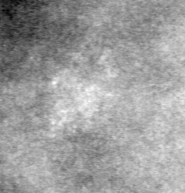
Crop from a digitized film mammogram around one marked abnormality, left breast, CC view, BI-RADS breast density category 4 (scale 1–4).
Finding: calcifications, morphology pleomorphic, distribution clustered; BI-RADS assessment category 4; subtlety rating 1 on a 1 (subtle) to 5 (obvious) scale; pathology result (as recorded, not read from the image): malignant.